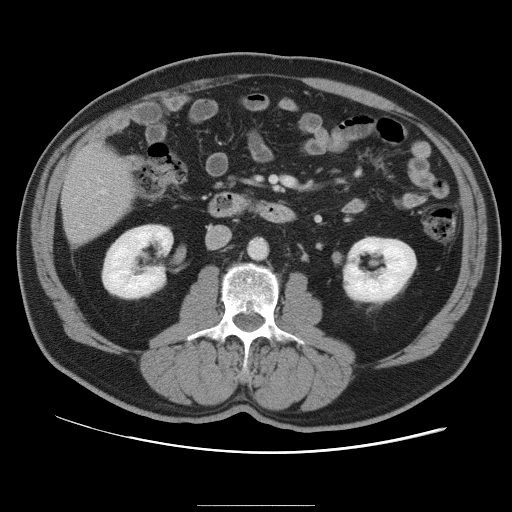
Contrast-enhanced abdominal CT, one axial slice; intravenous contrast given; soft-tissue window (W 400 / L 40 HU); 5 mm slice thickness; 512 × 512 image matrix, field of view 399 × 399 mm. Male patient, age 64 years. Case-level facts recorded for this patient, not image findings: diagnosis: colorectal cancer liver metastases, imaged before liver resection; multiple liver metastases: yes; largest metastasis: 3 cm; disease in both lobes: yes.
Structures marked on this image (expert manual segmentation):
- hepatic veins: box from (x=101, y=190) to (x=106, y=194) px
- liver: (x=64, y=148)–(x=132, y=243)
- planned liver remnant (the part of the liver to remain after resection): (x=64, y=148)–(x=132, y=231)